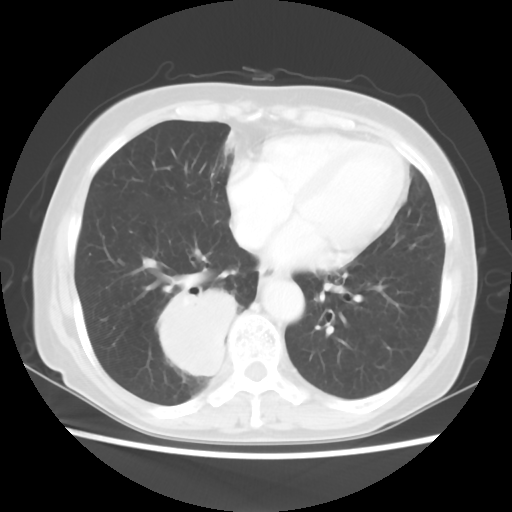
Chest CT, one axial slice. Position 20 of 56 along the scan axis. Reconstruction kernel STANDARD. Lung window (W 1500 / L -600 HU). 5 mm slice thickness. 512 × 512 image matrix. Patient: female, 66 years. Case-level facts recorded for this patient, not image findings: clinical TNM (as recorded): T2 N3 M0; histopathological grade: G3.
Outlined on this slice (rectangle marked by the reading radiologist):
- lung tumour (recorded histology: small cell carcinoma): box from (x=149, y=276) to (x=245, y=388) px